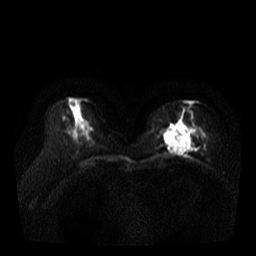
Breast MRI, one axial slice. Position 15 of 35 along the scan axis. Diffusion-weighted series; image 2 of 4 stored at this slice position (different b-values; order by instance number). 3 T. 5 mm slice thickness. 256 × 256 image matrix, field of view 320 × 320 mm. Female patient.
Outlined on this slice (outlined manually by an expert reader):
- tumour on diffusion-weighted imaging: bounding box (x1, y1, x2, y2) in pixels: (163, 131, 190, 153)